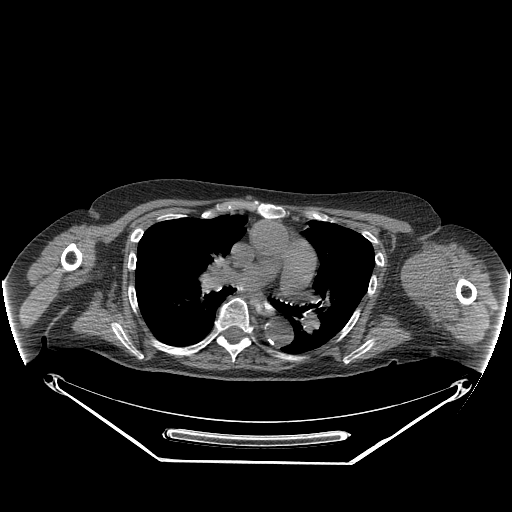
CT of an extremity soft-tissue mass (from a PET/CT study), one axial slice; position 180 of 267 along the scan axis; 140 kVp; soft-tissue window (W 400 / L 40 HU); 3.75 mm slice thickness; 512 × 512 image matrix. Female patient. Case-level facts recorded for this patient, not image findings: histological type: pleiomorphic leiomyosarcoma; grade: high; site of the primary tumour: left biceps.
Outlined on this slice (expert contour drawn on MRI and transferred to this co-registered scan by the dataset authors):
- gross tumour volume including surrounding oedema: bounding box (x1, y1, x2, y2) in pixels: (409, 249, 455, 320)
- gross tumour volume (mass): (409, 249, 453, 305)